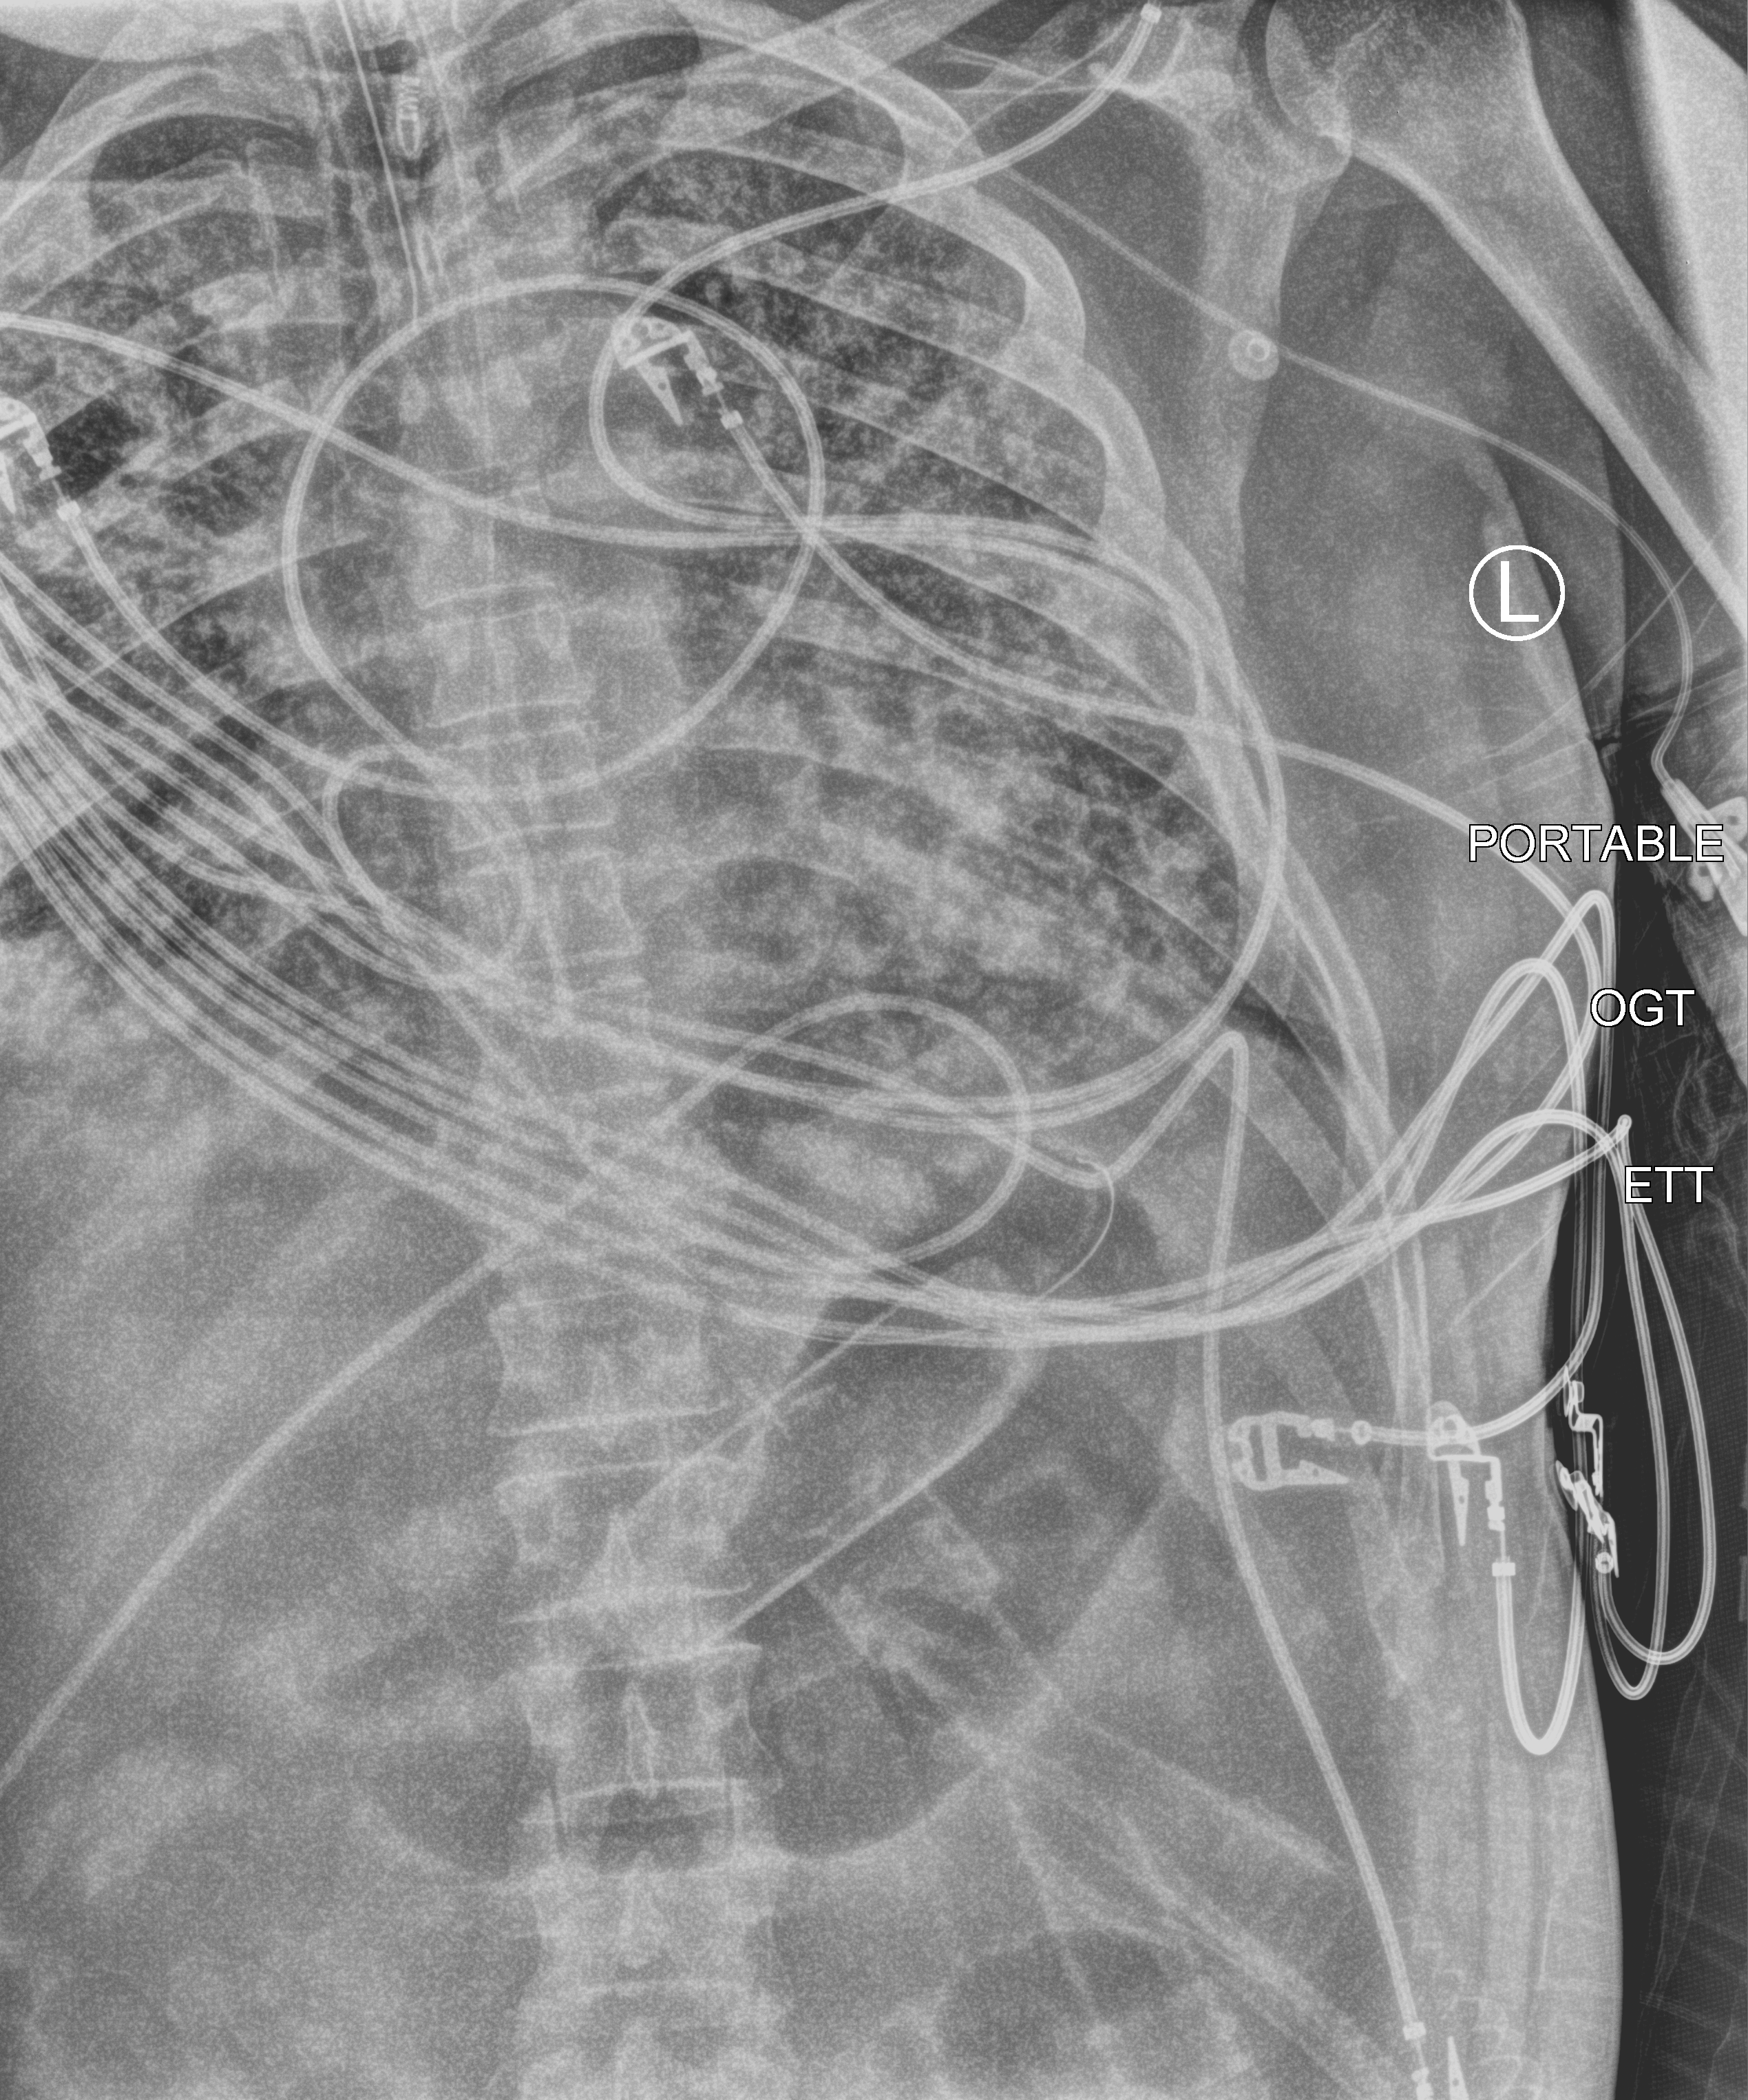
Portable chest radiograph. Male patient hospitalised with COVID-19, age 18–59 years.
Hospital-stay facts (about this admission, not read from this image; timing relative to this image not recorded):
- admitted to intensive care during this hospital stay: yes
- COPD (admission record): no